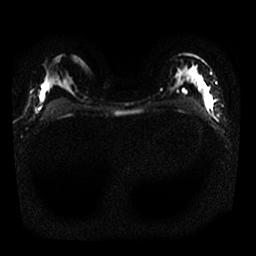
Breast MRI, one axial slice. Slice 16 of 25 in the series (ordered by position). Diffusion-weighted series; image 2 of 4 stored at this slice position (different b-values; order by instance number). 1.5 T. 4 mm slice thickness. 256 × 256 image matrix, field of view 320 × 320 mm. Female patient.
Annotated regions visible in this slice (outlined manually by an expert reader):
- tumour on diffusion-weighted imaging: bounding box (x1, y1, x2, y2) in pixels: (198, 79, 213, 108)